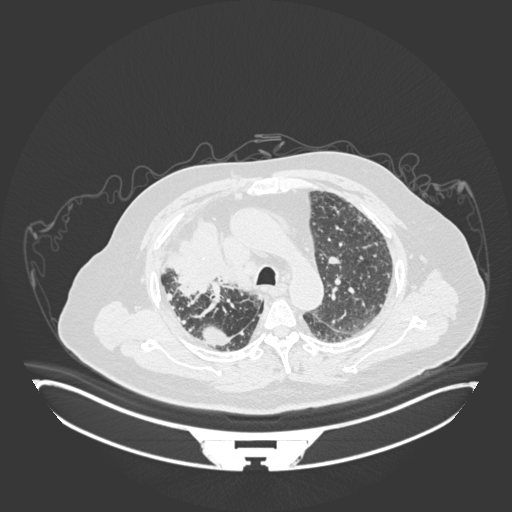
Chest CT, one axial slice. Position 129 of 201 along the scan axis. Reconstruction kernel B30f. Lung window (W 1500 / L -600 HU). 1 mm slice thickness. 512 × 512 image matrix. Patient: male, 69 years. Case-level facts recorded for this patient, not image findings: clinical TNM (as recorded): T4 N3 M1.
Outlined on this slice (rectangle marked by the reading radiologist):
- lung tumour (recorded histology: adenocarcinoma): bounding box [x1, y1, x2, y2] px = [171, 206, 234, 301]